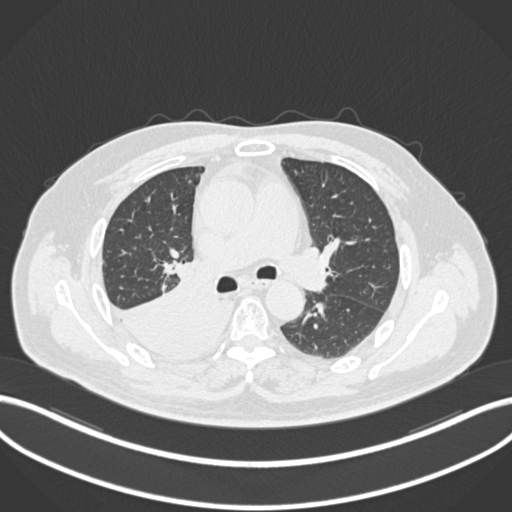
Chest CT, one axial slice; position 119 of 218 along the scan axis; reconstruction kernel B30f; lung window (W 1500 / L -600 HU); 1 mm slice thickness; 512 × 512 image matrix, field of view 400 × 400 mm. Male patient, age 68 years. Case-level facts recorded for this patient, not image findings: clinical TNM (as recorded): T2a N0 M0.
Annotated regions visible in this slice (rectangle marked by the reading radiologist):
- lung tumour (recorded histology: adenocarcinoma): bounding box [x1, y1, x2, y2] px = [106, 281, 235, 372]